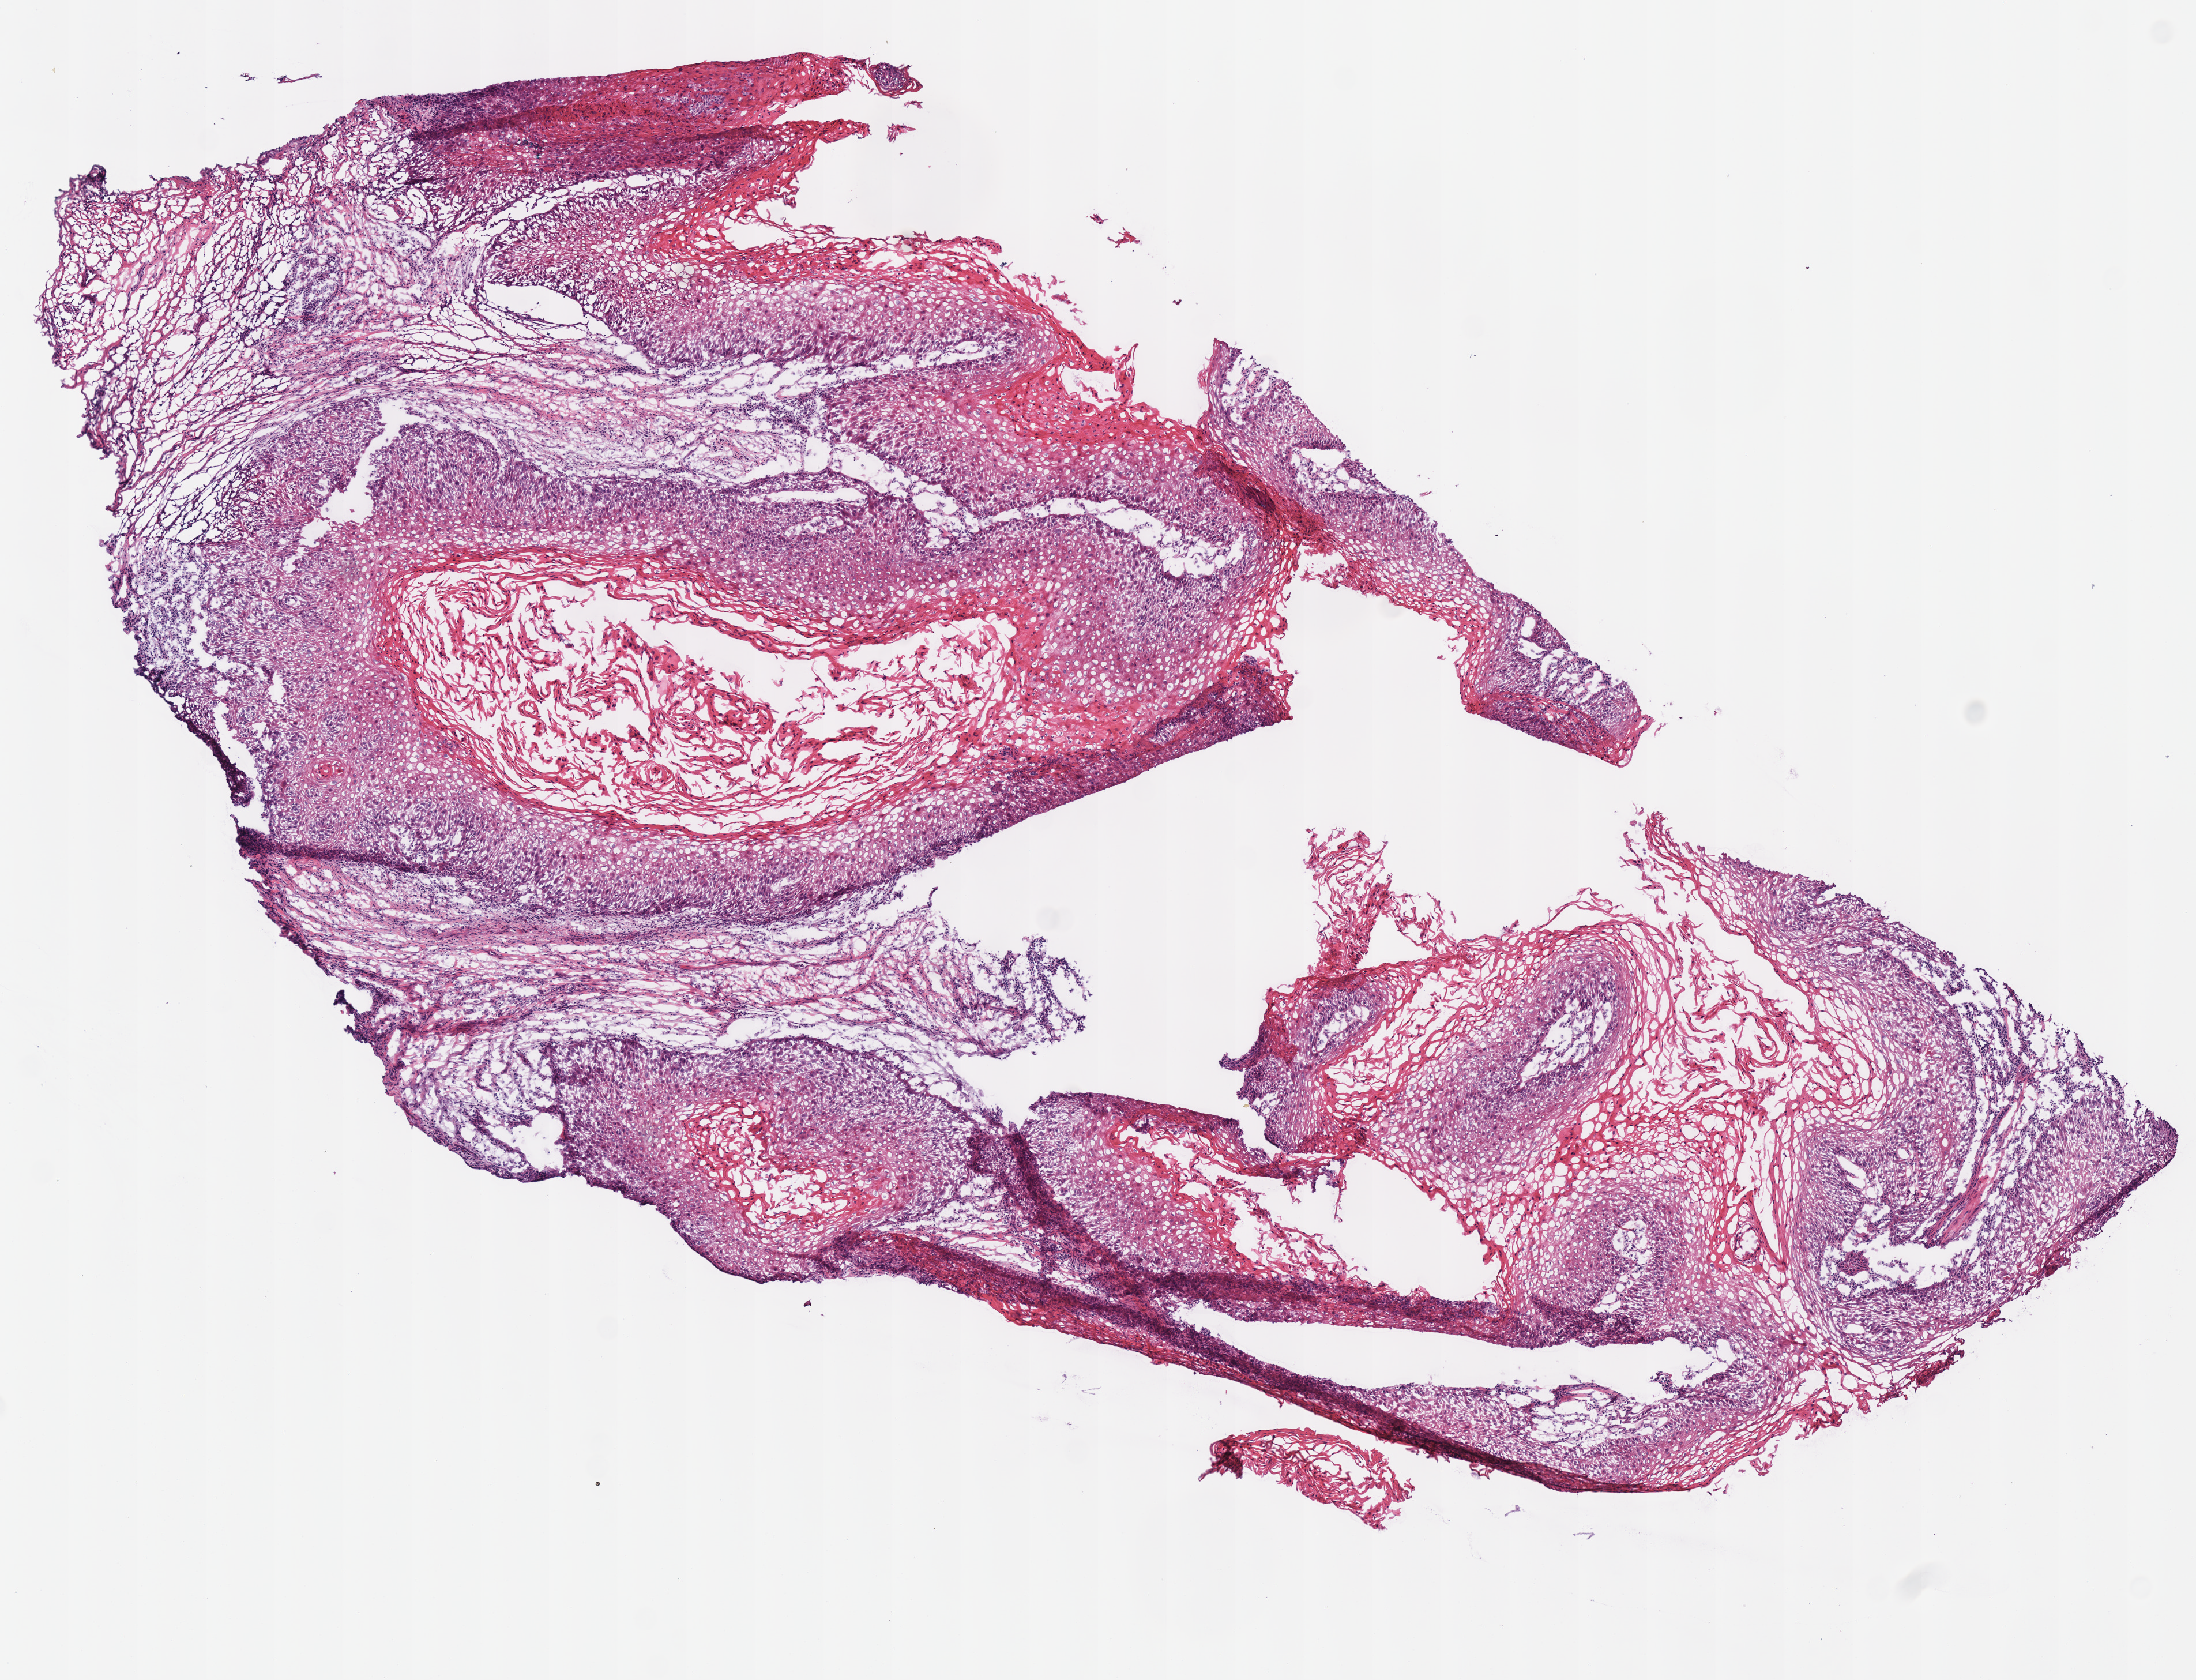
Digitized Hematoxylin and eosin (H&E) stained tissue section (whole slide) — low-resolution overview of the scanned area, about 7.5 x 5.7 mm. Frozen section from the top of the tissue portion. Sample: primary tumour, head and neck. Female patient; age at initial diagnosis 77 years. Histologic grade: G1 (well differentiated). Slide review estimates, as recorded: tumour cells 100%, tumour nuclei 80%, normal cells 0%, stromal cells 0%, necrosis 0%. Inflammatory infiltration, as recorded: lymphocyte infiltration 12%, monocyte infiltration 0%, neutrophil infiltration 0%.
- diagnosis: Squamous cell carcinoma, NOS (overlapping lesion of lip, oral cavity and pharynx)
- AJCC pathologic stage: III (7th edition)